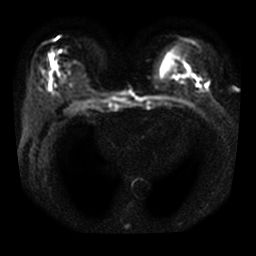
Breast MRI, one axial slice; position 18 of 33 along the scan axis; diffusion-weighted series; image 2 of 4 stored at this slice position (different b-values; order by instance number); 3 T; 5 mm slice thickness; 256 × 256 image matrix, field of view 320 × 320 mm. Female patient.
Outlined on this slice (expert manual segmentation):
- tumour on diffusion-weighted imaging: box from (x=192, y=74) to (x=208, y=86) px